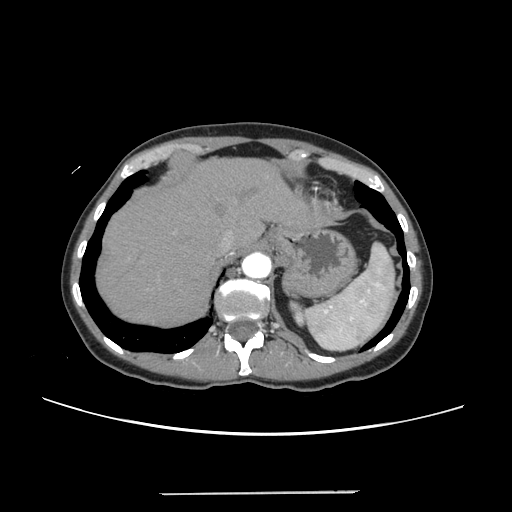
Contrast-enhanced abdominal CT, one axial slice. Position 200 of 240 along the scan axis. 120 kVp. Intravenous contrast given. Soft-tissue window (W 400 / L 40 HU). 512 × 512 image matrix, field of view 371 × 371 mm. Female patient, age 60 years. Case-level facts recorded for this patient, not image findings: diagnosis: colorectal cancer liver metastases, imaged before liver resection; multiple liver metastases: no; largest metastasis: 1.5 cm; disease in both lobes: no.
Outlined on this slice (expert manual segmentation):
- hepatic veins: bounding box [x1, y1, x2, y2] px = [218, 218, 250, 252]
- liver: [97, 159, 323, 326]
- planned liver remnant (the part of the liver to remain after resection): [97, 159, 321, 326]